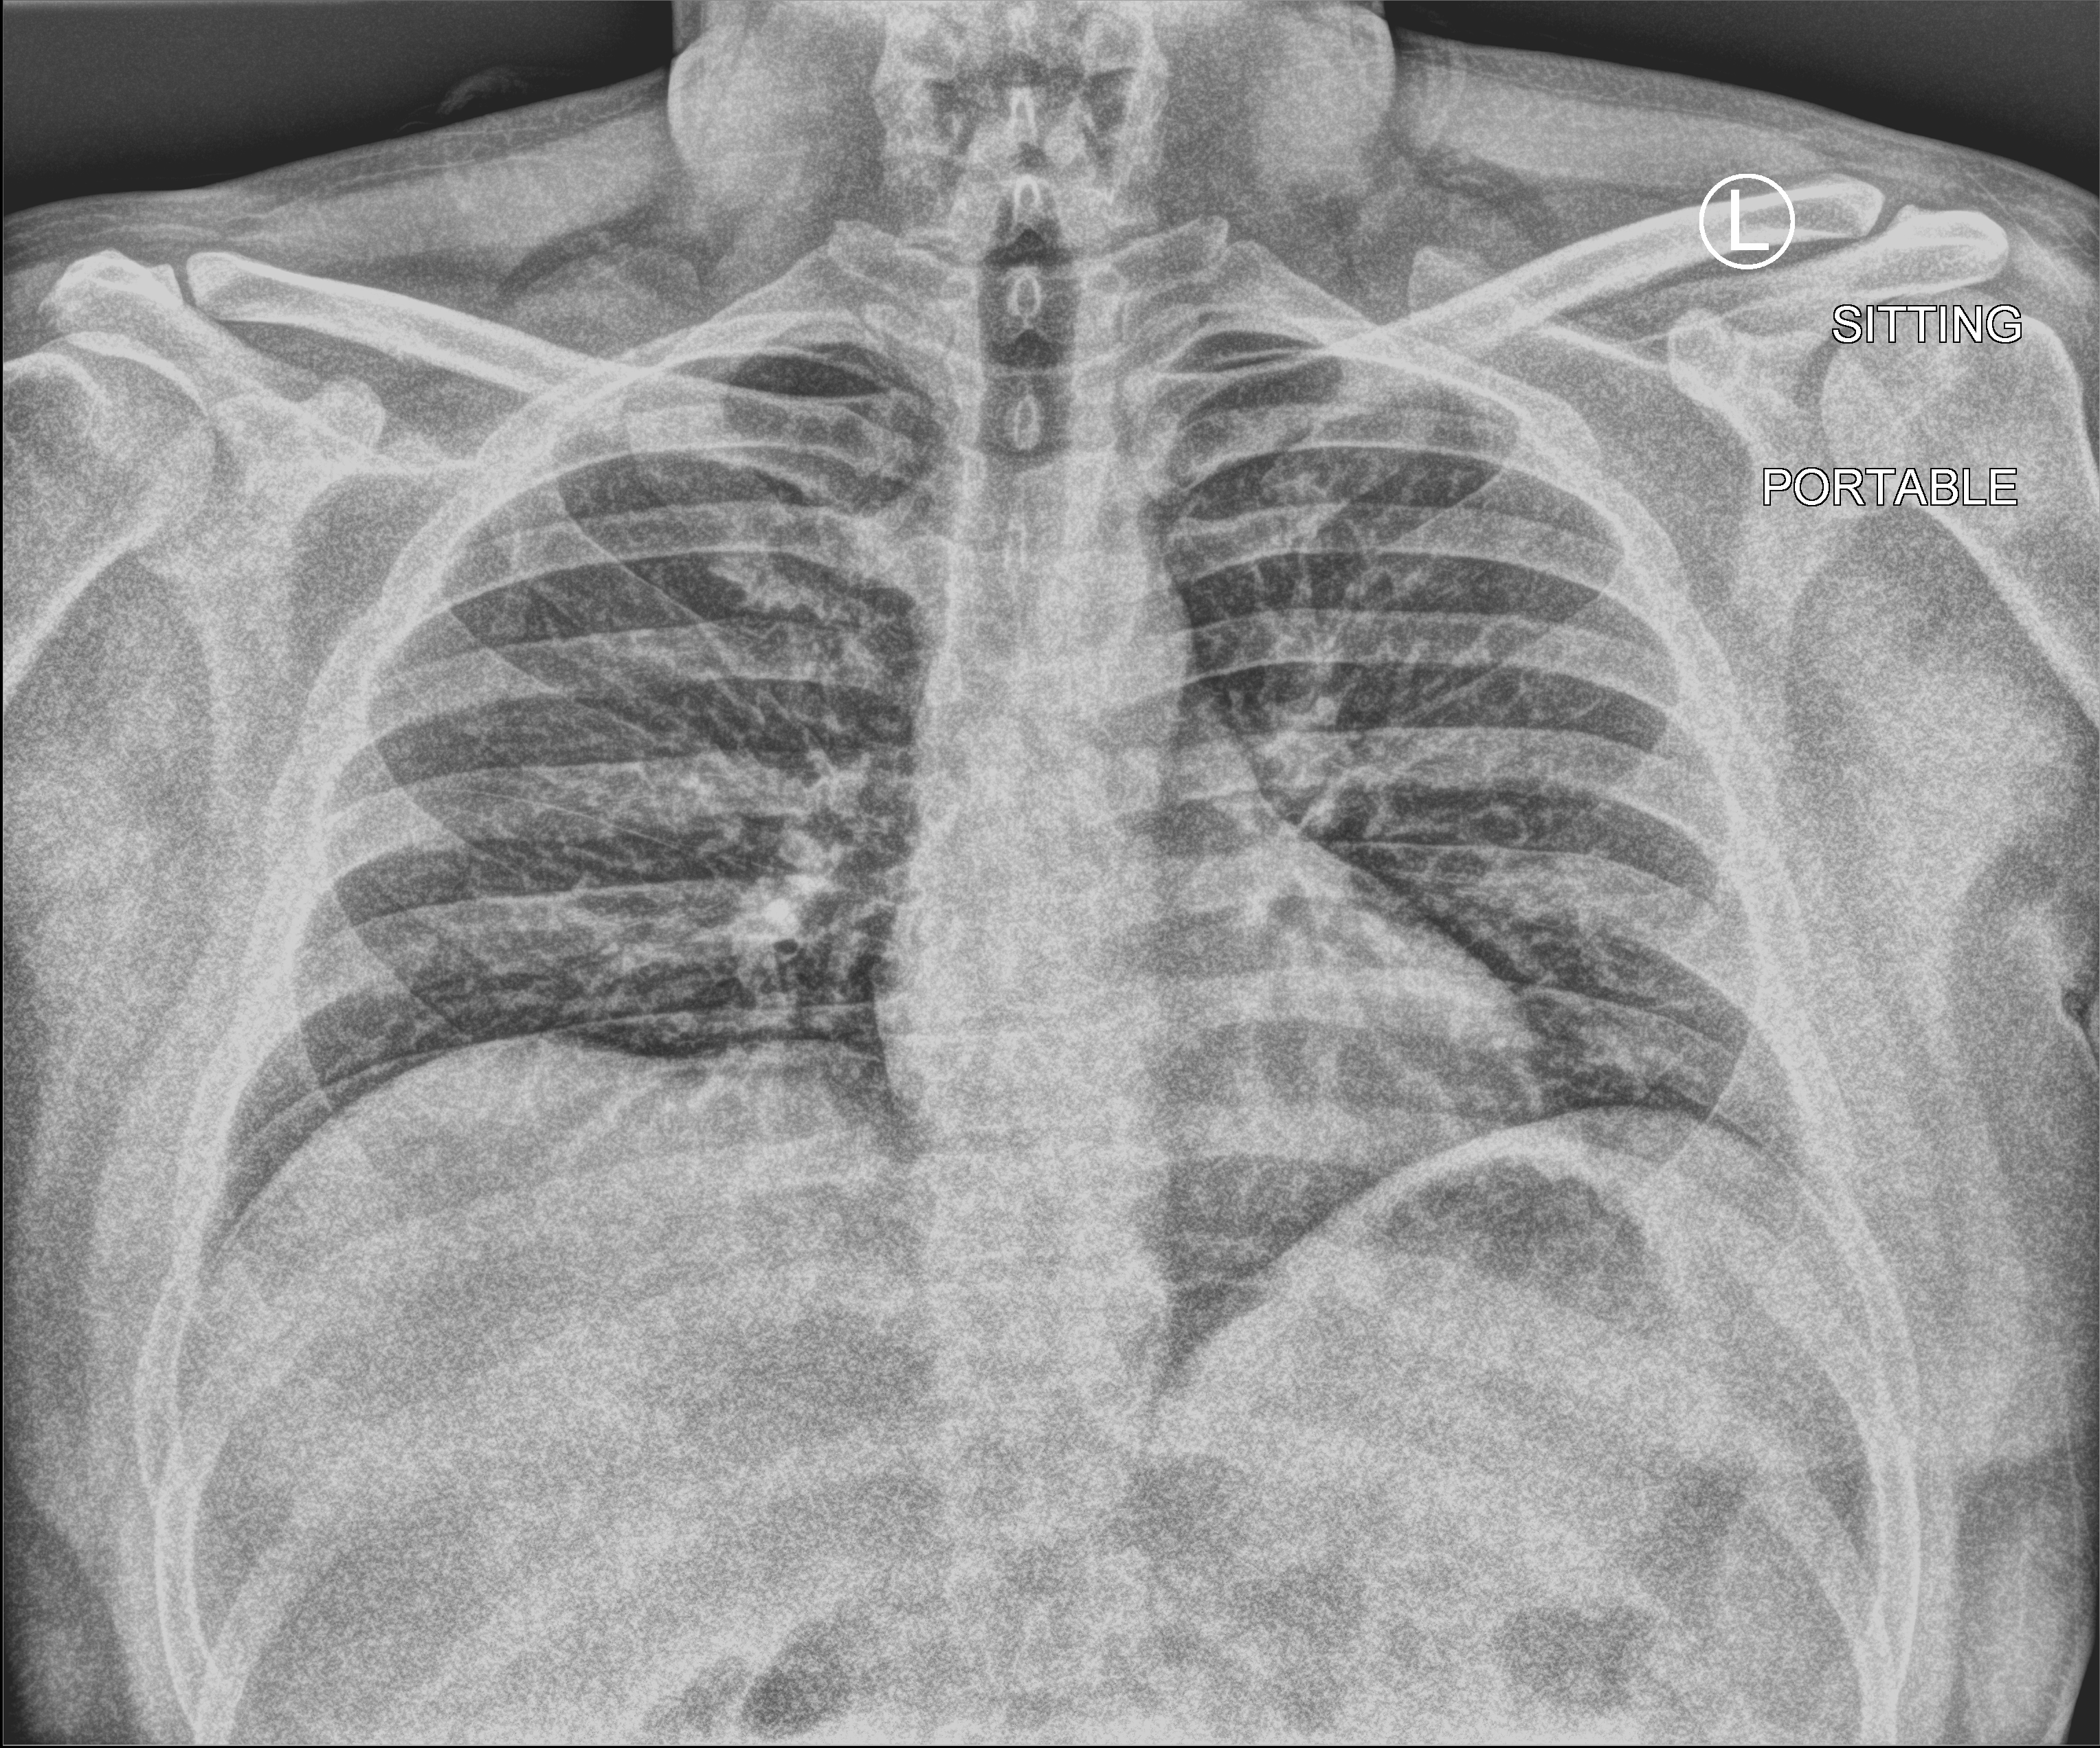
Portable chest radiograph, anteroposterior (AP) projection. Patient hospitalised with COVID-19; male, aged 18–59 years.
Hospital-stay facts (about this admission, not read from this image; timing relative to this image not recorded): admitted to intensive care during this hospital stay: no.